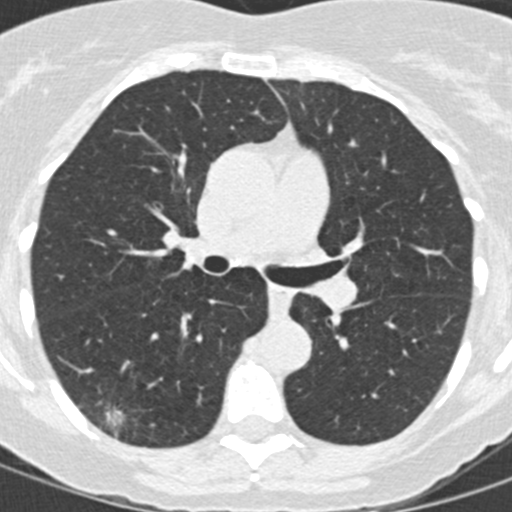
Low-dose screening chest CT, one axial slice; slice 85 of 146 in the series (ordered by position); lung window (W 1500 / L -600 HU); 512 × 512 image matrix, field of view 270 × 270 mm.
Annotated regions visible in this slice (expert manual segmentation):
- lesion 1 (tumor, lower lobe of right lung): bounding box [x1, y1, x2, y2] px = [106, 409, 124, 427]